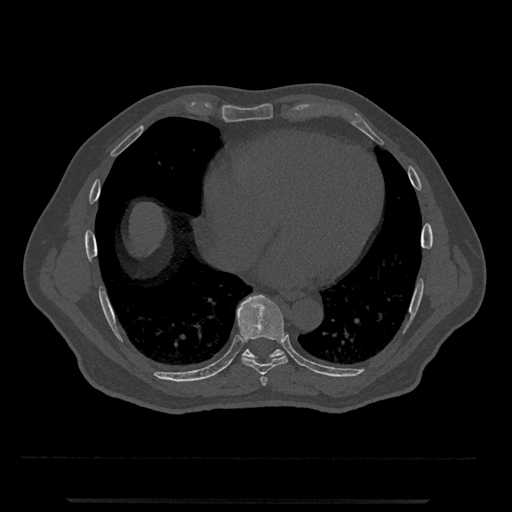
CT including the spine, one axial slice; position 611 of 797 along the scan axis; bone window (W 1800 / L 400 HU); 512 × 512 image matrix, field of view 419 × 419 mm. Patient: male, 63 years. From the clinical record (not read from this slice): primary cancer: prostate.
Outlined on this slice (semi-automatic segmentation, software-assisted and operator-edited):
- T7 vertebra: bounding box (x1, y1, x2, y2) in pixels: (260, 376, 267, 386)
- T8 vertebra: (237, 295, 288, 375)
- T9 vertebra: (242, 349, 284, 362)